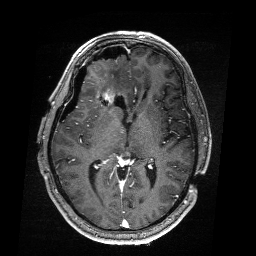
Brain MRI from a brain-tumour surgery series, one axial slice; position 105 of 176 along the scan axis; T1-weighted post-contrast; 1 mm slice thickness; 256 × 256 image matrix. Case-level facts recorded for this patient, not image findings: histopathology: Astrocytoma; WHO grade: 4; IDH mutation: yes.
Annotated regions visible in this slice (outlined manually by an expert reader):
- residual tumour: bounding box [x1, y1, x2, y2] px = [90, 85, 119, 99]